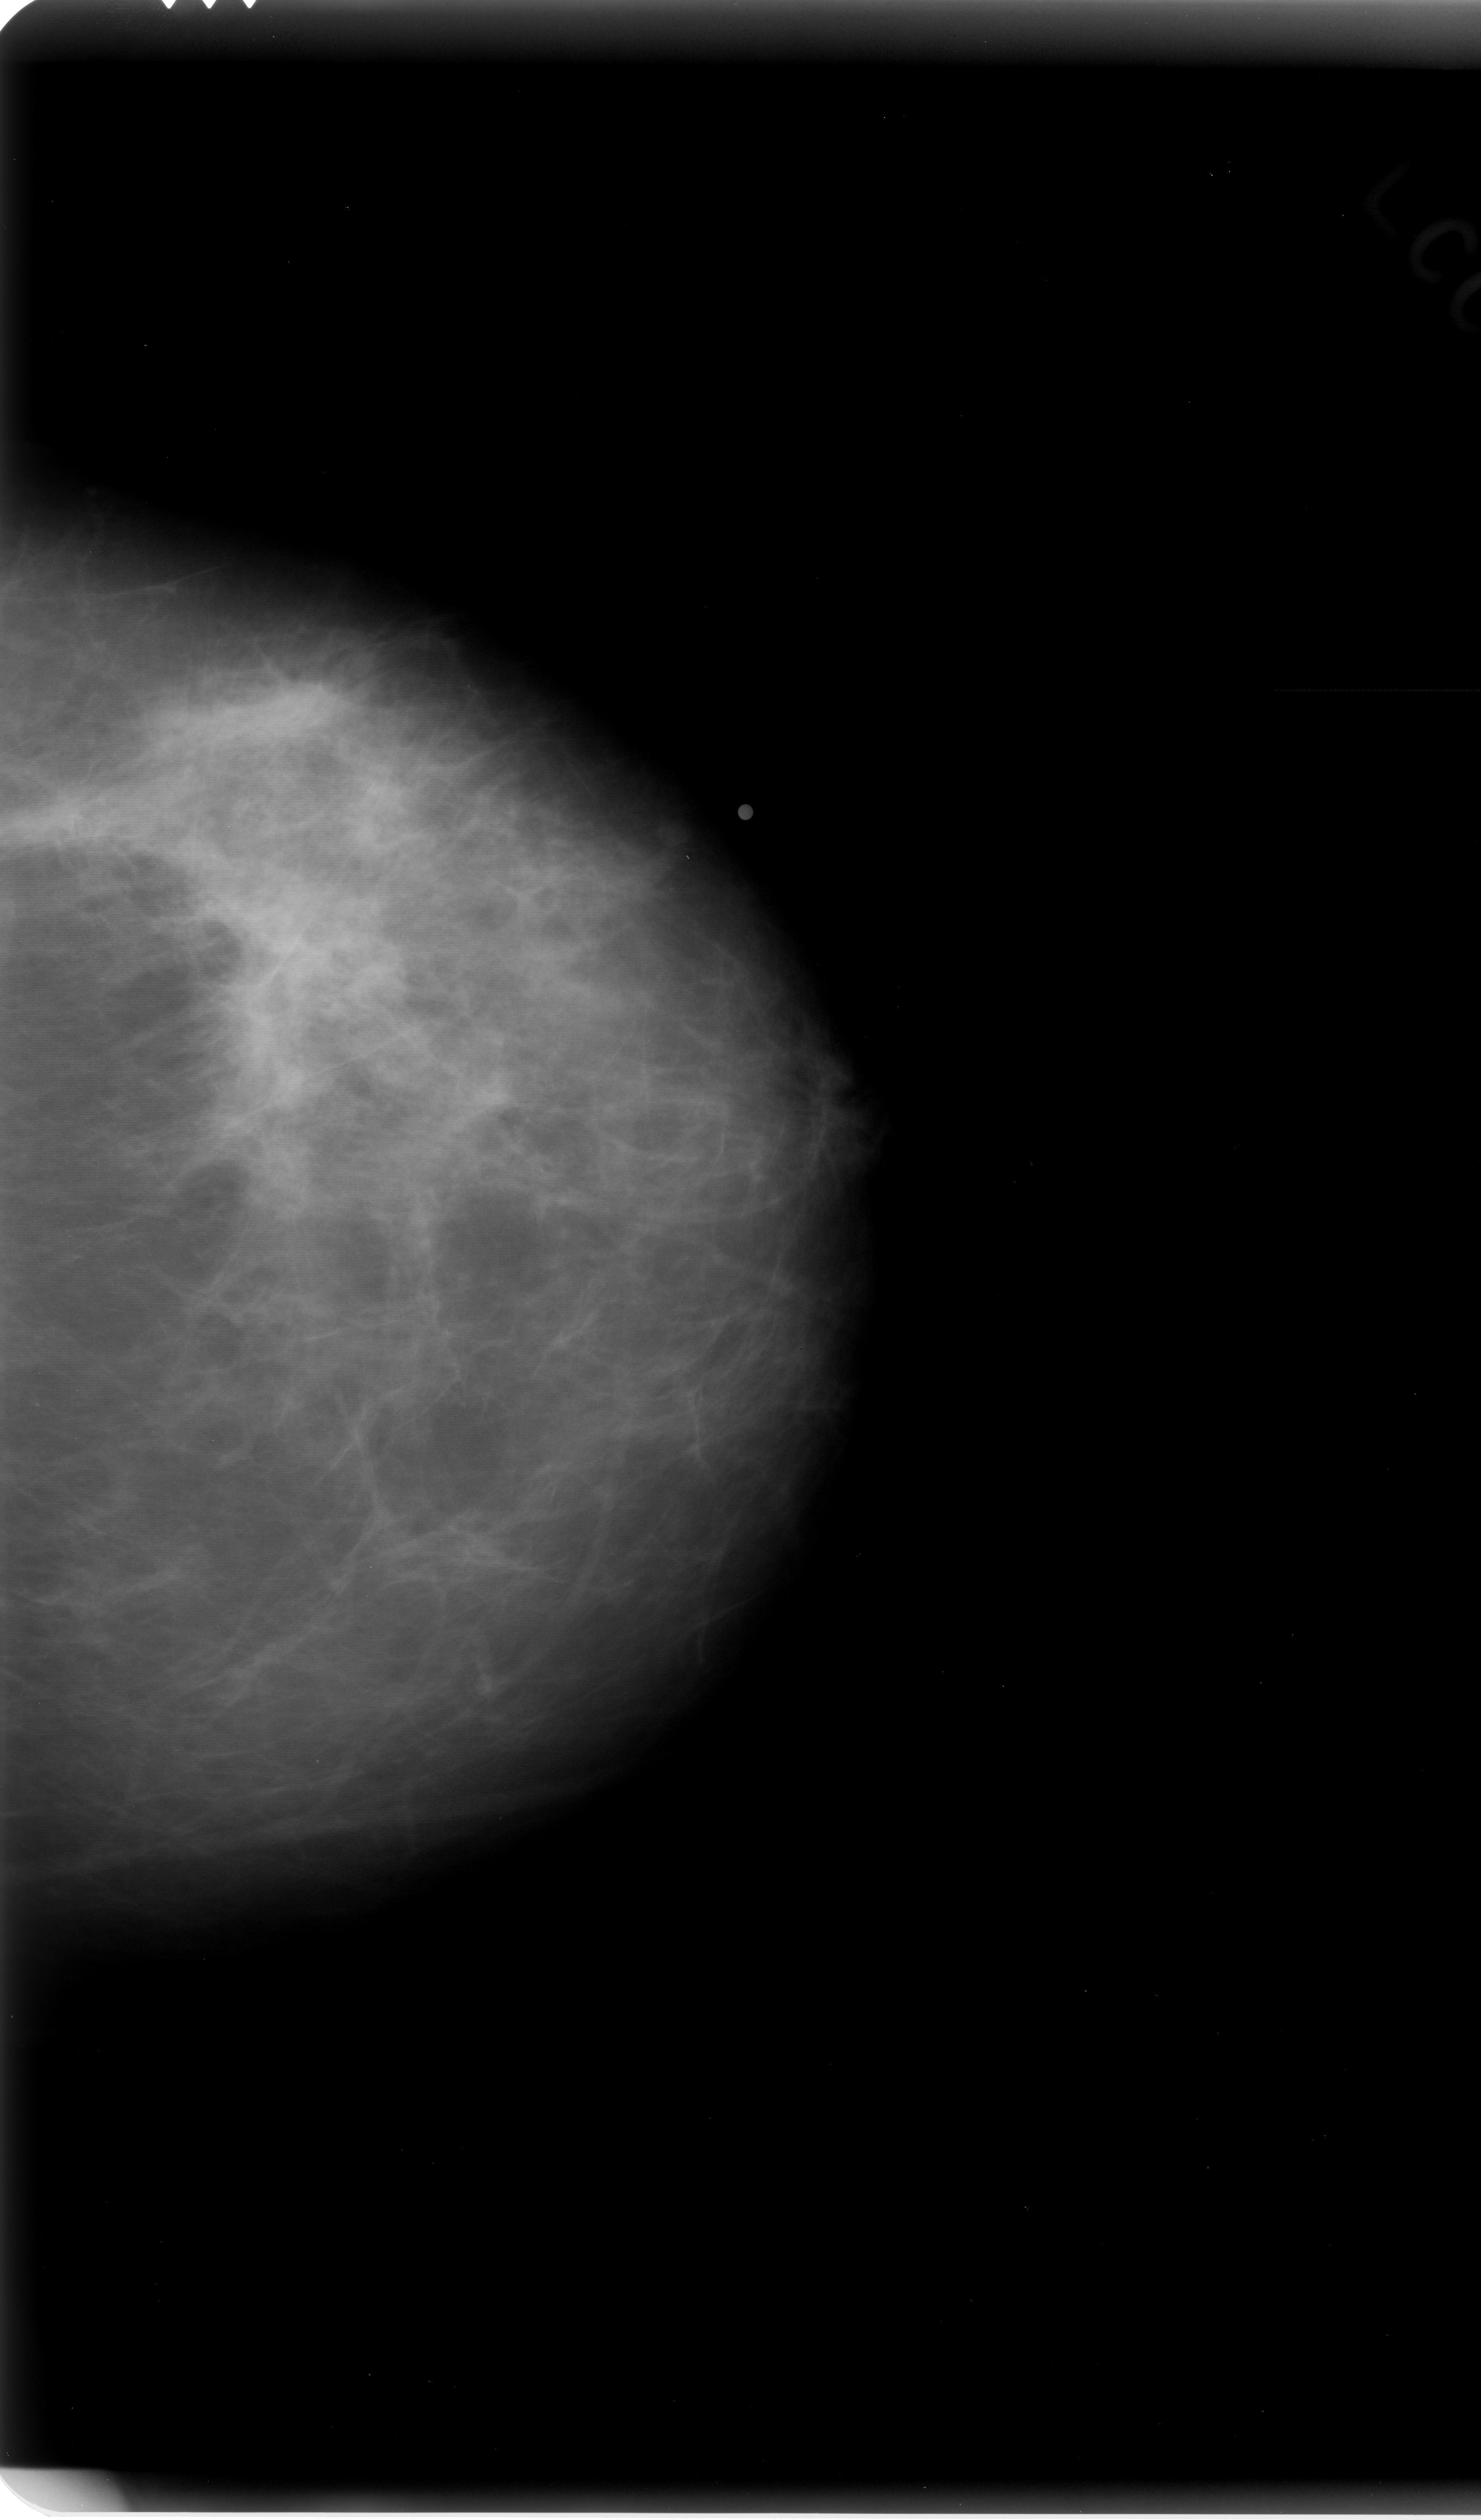
Mammogram (digitized film); left breast; craniocaudal (CC) view; BI-RADS breast density category 1 (scale 1–4); 1481 × 2520 image matrix.
Marked abnormalities (boxes around the expert regions of interest):
- mass, shape irregular, margins spiculated; BI-RADS assessment category 5; pathology result (as recorded, not read from the image): malignant: bounding box [x1, y1, x2, y2] px = [184, 853, 427, 1090]